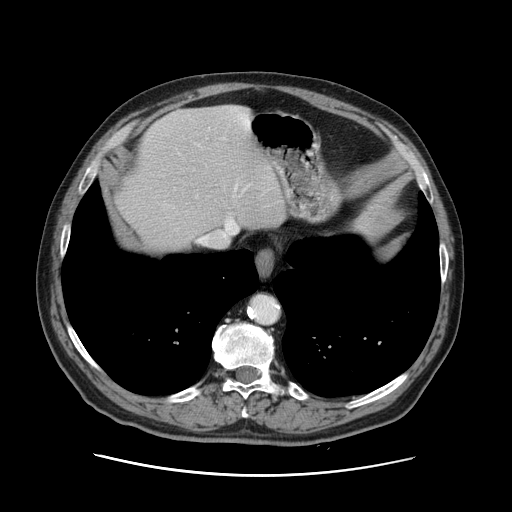
Contrast-enhanced abdominal CT, one axial slice; slice 111 of 141 in the series (ordered by position); soft-tissue window (W 400 / L 40 HU); 2.5 mm slice thickness; 512 × 512 image matrix. Male patient, age 72 years. From the clinical record (not read from this slice): diagnosis: colorectal cancer liver metastases, imaged before liver resection; multiple liver metastases: yes; largest metastasis: 5.4 cm.
Annotated regions visible in this slice (manually delineated by an expert):
- hepatic veins: box from (x=209, y=129) to (x=250, y=235) px
- liver: (x=117, y=105)–(x=284, y=250)
- planned liver remnant (the part of the liver to remain after resection): (x=148, y=105)–(x=284, y=250)